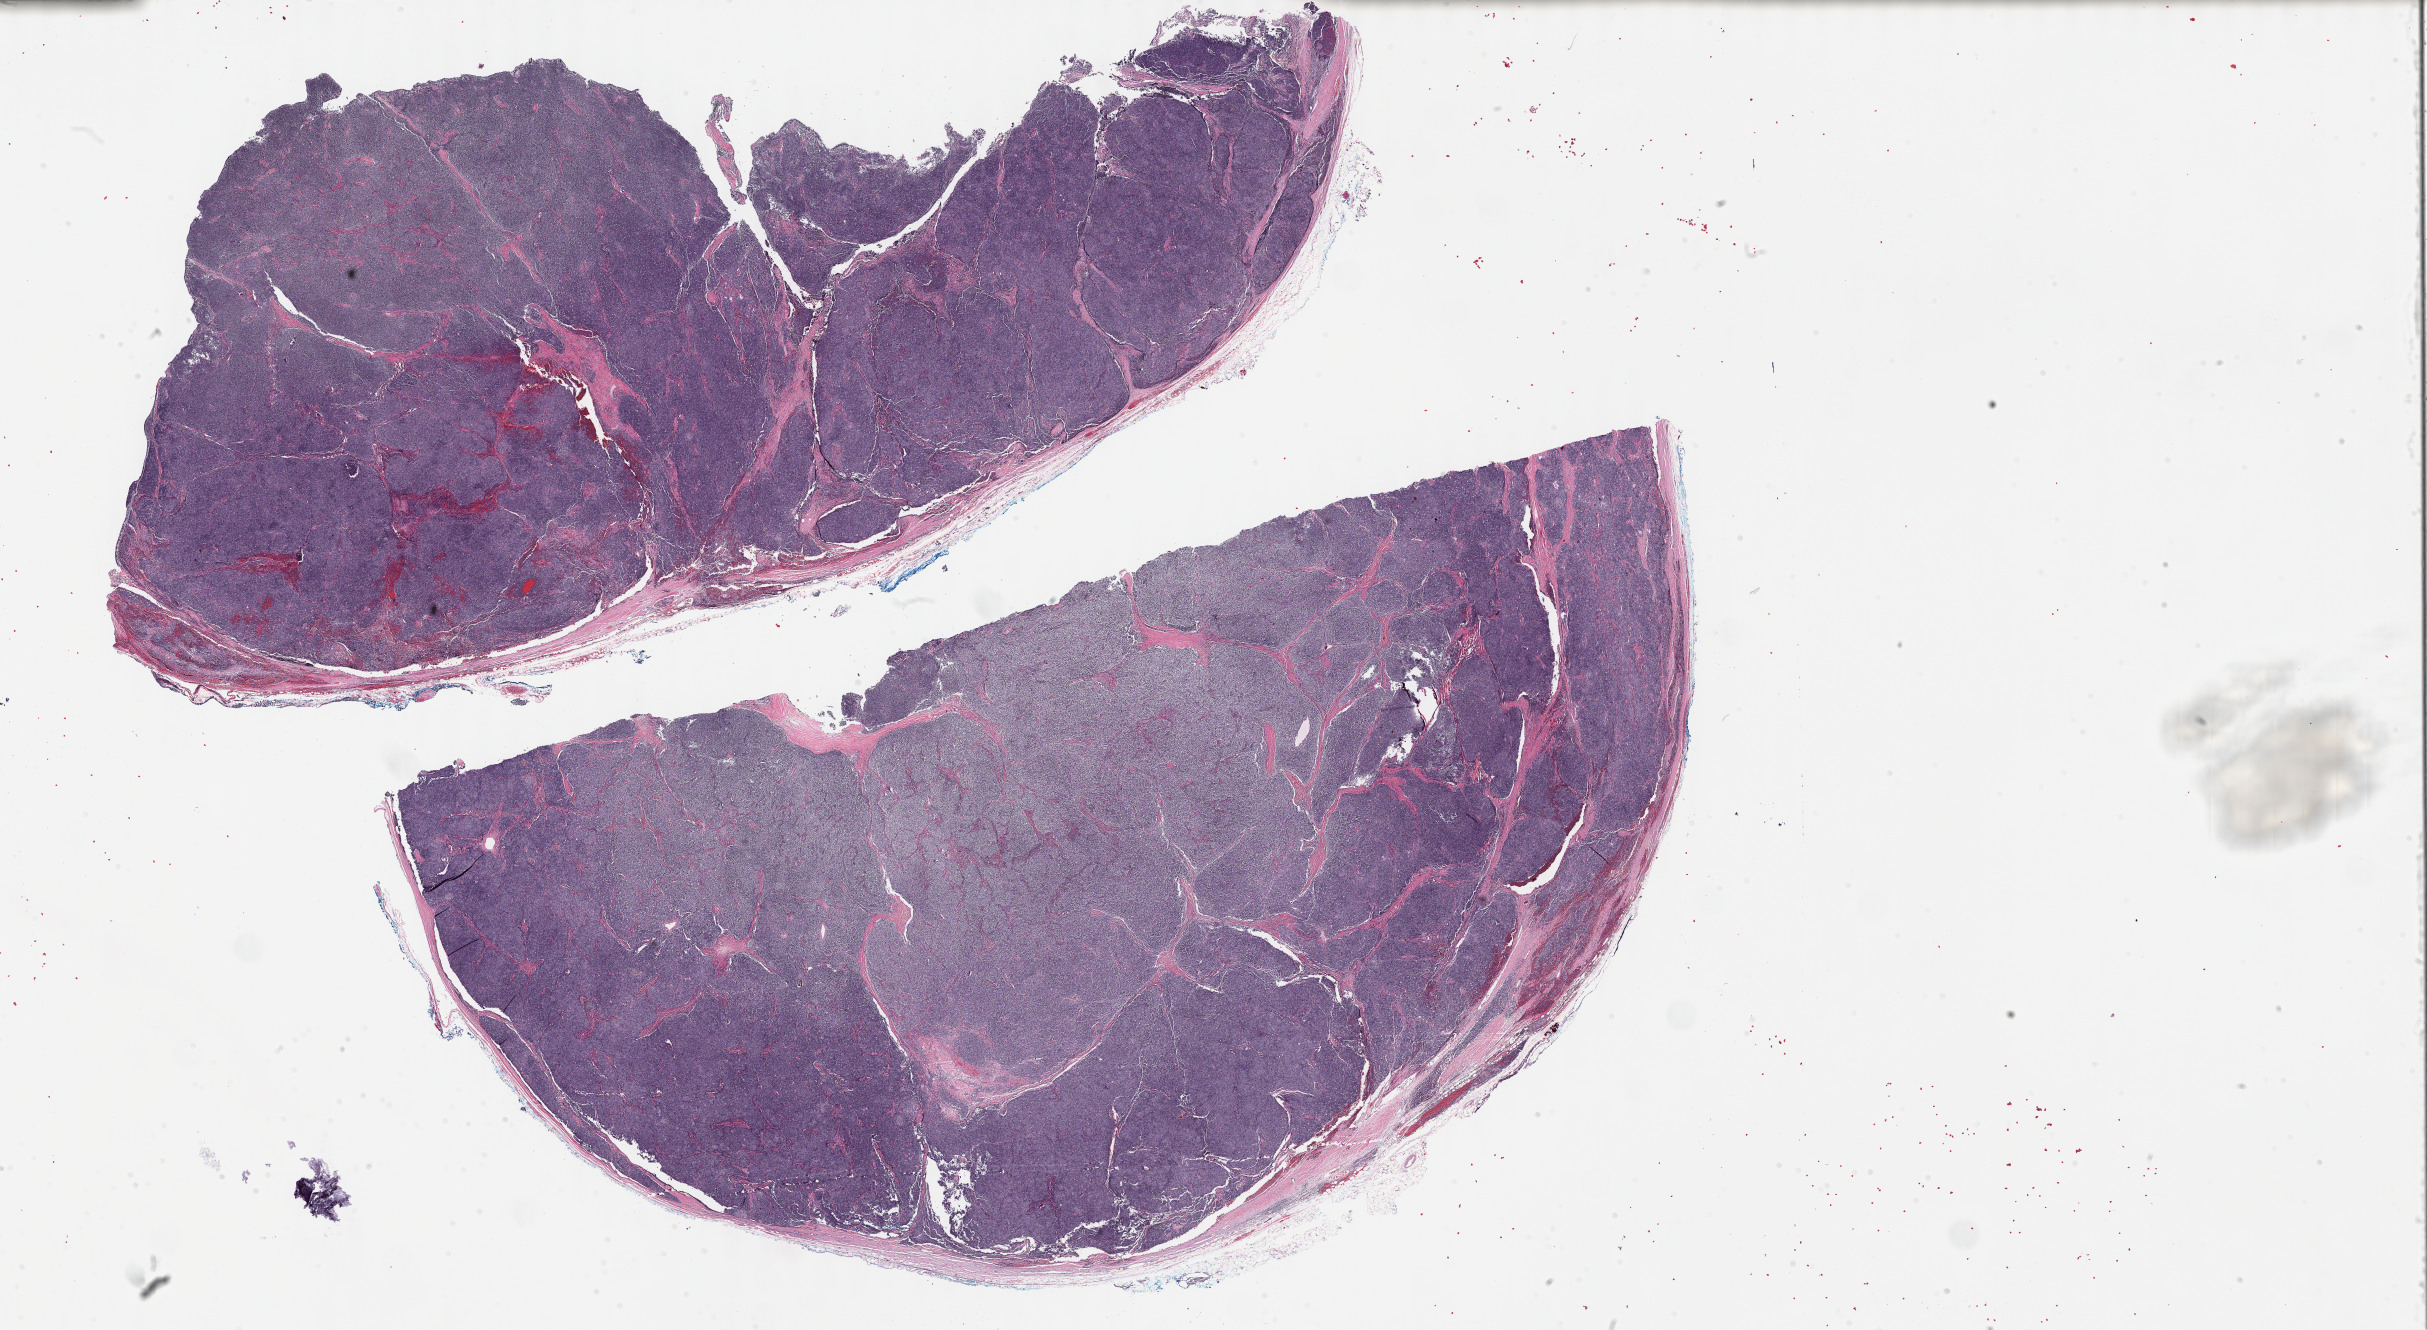
Digitized Hematoxylin and eosin (H&E) stained tissue section (whole slide) — low-resolution overview of the scanned area, about 39.3 x 21.5 mm (slide scanned at 40x); formalin-fixed paraffin-embedded (FFPE) diagnostic section; thymus, primary tumour sample. Patient: female, age at initial diagnosis 60 years.
- pathologic diagnosis: Thymoma, type B1, malignant